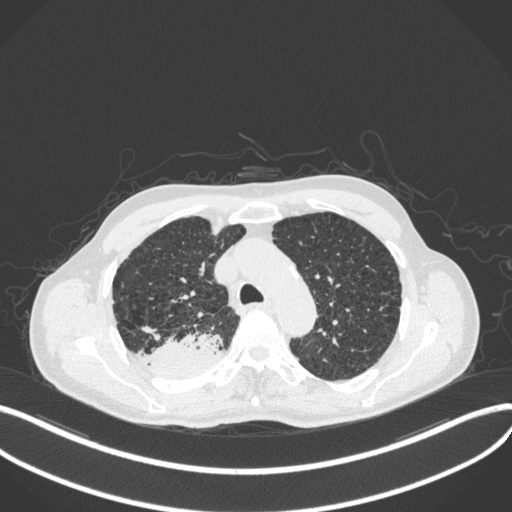
Chest CT, one axial slice; position 329 of 423 along the scan axis; 120 kVp; lung window (W 1500 / L -600 HU); 512 × 512 image matrix, field of view 400 × 400 mm. Male patient, age 79 years. Case-level facts recorded for this patient, not image findings: clinical TNM (as recorded): T3 N0 M0.
Outlined on this slice (rectangle marked by the reading radiologist):
- lung tumour (recorded histology: adenocarcinoma): bounding box <148,331,224,378> (left, top, right, bottom; pixels)